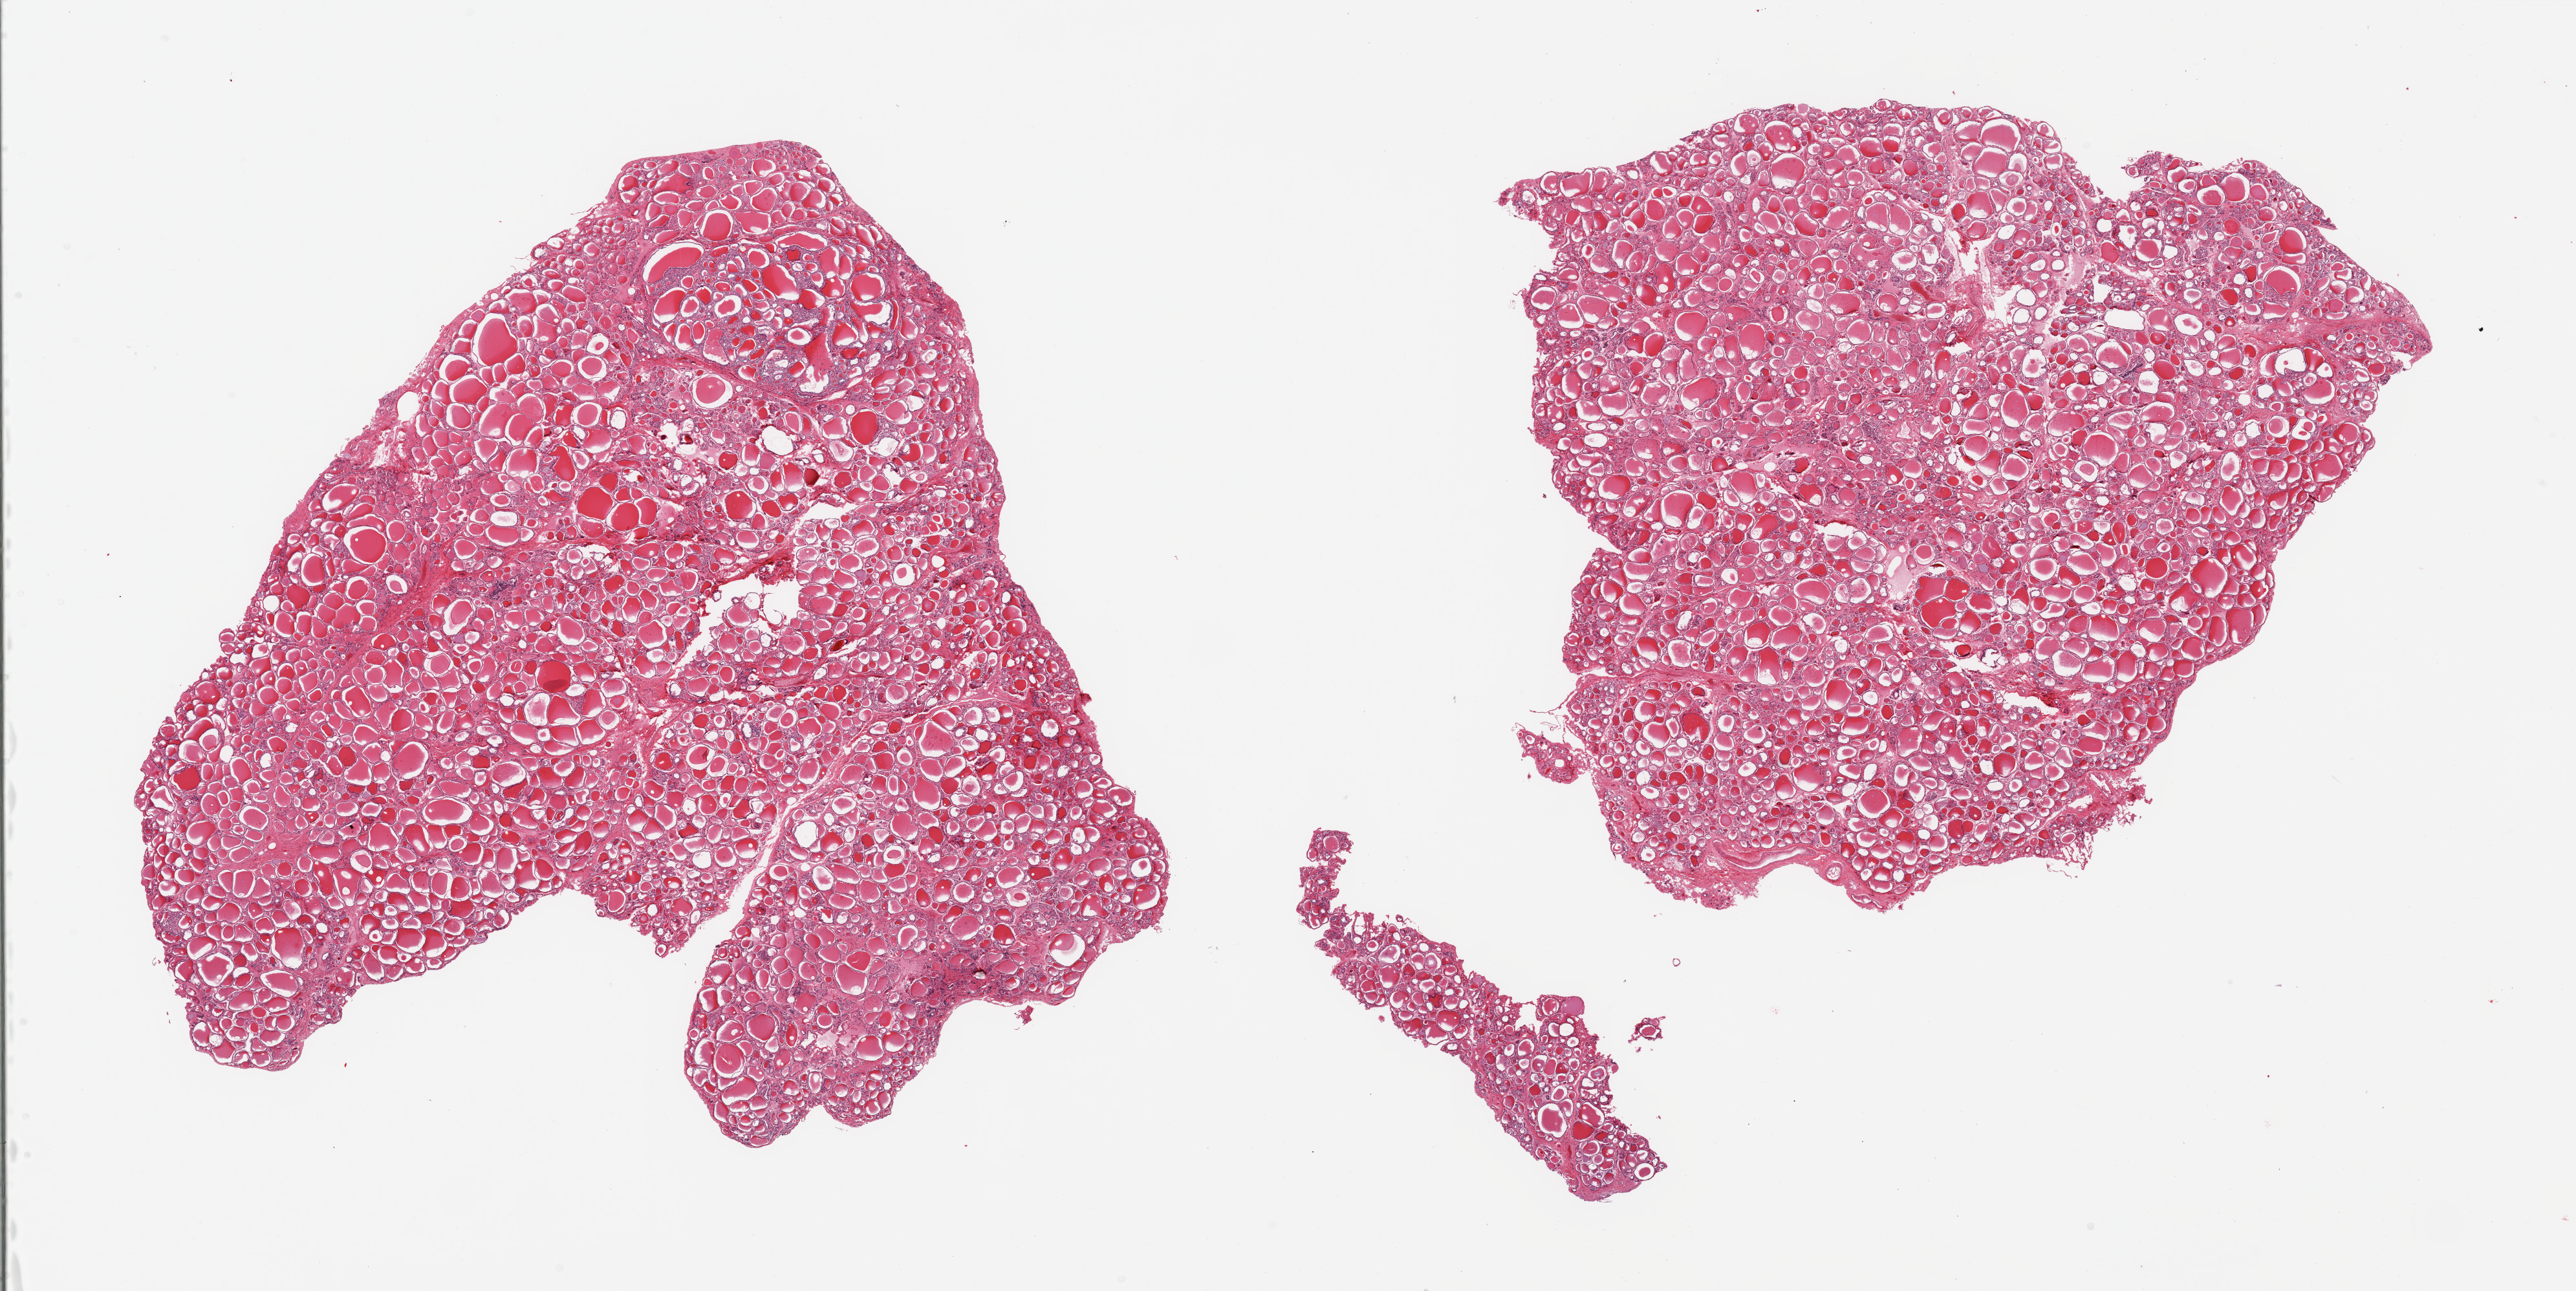
Haematoxylin and eosin whole-slide image, brightfield, whole scanned area (about 31.5 x 15.8 mm, acquisition: 20x scan) shown as a low-resolution overview; PAXgene-fixed paraffin-embedded (PFPE) section; section of thyroid (target tissue); donor tissue sample. Donor sex: female.
Reviewer comment on this tissue sample: 2 pieces; well dissected.